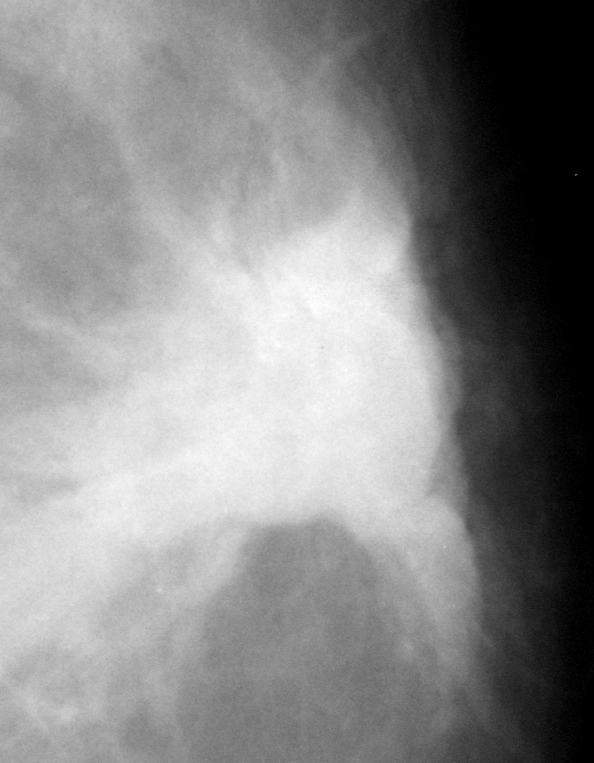
Region of interest cut from a scanned film mammogram (one marked finding), left breast, CC view, BI-RADS breast density category 2 (scale 1–4).
- Finding: mass, shape irregular, margins spiculated; BI-RADS assessment category 5; pathology result (as recorded, not read from the image): malignant.